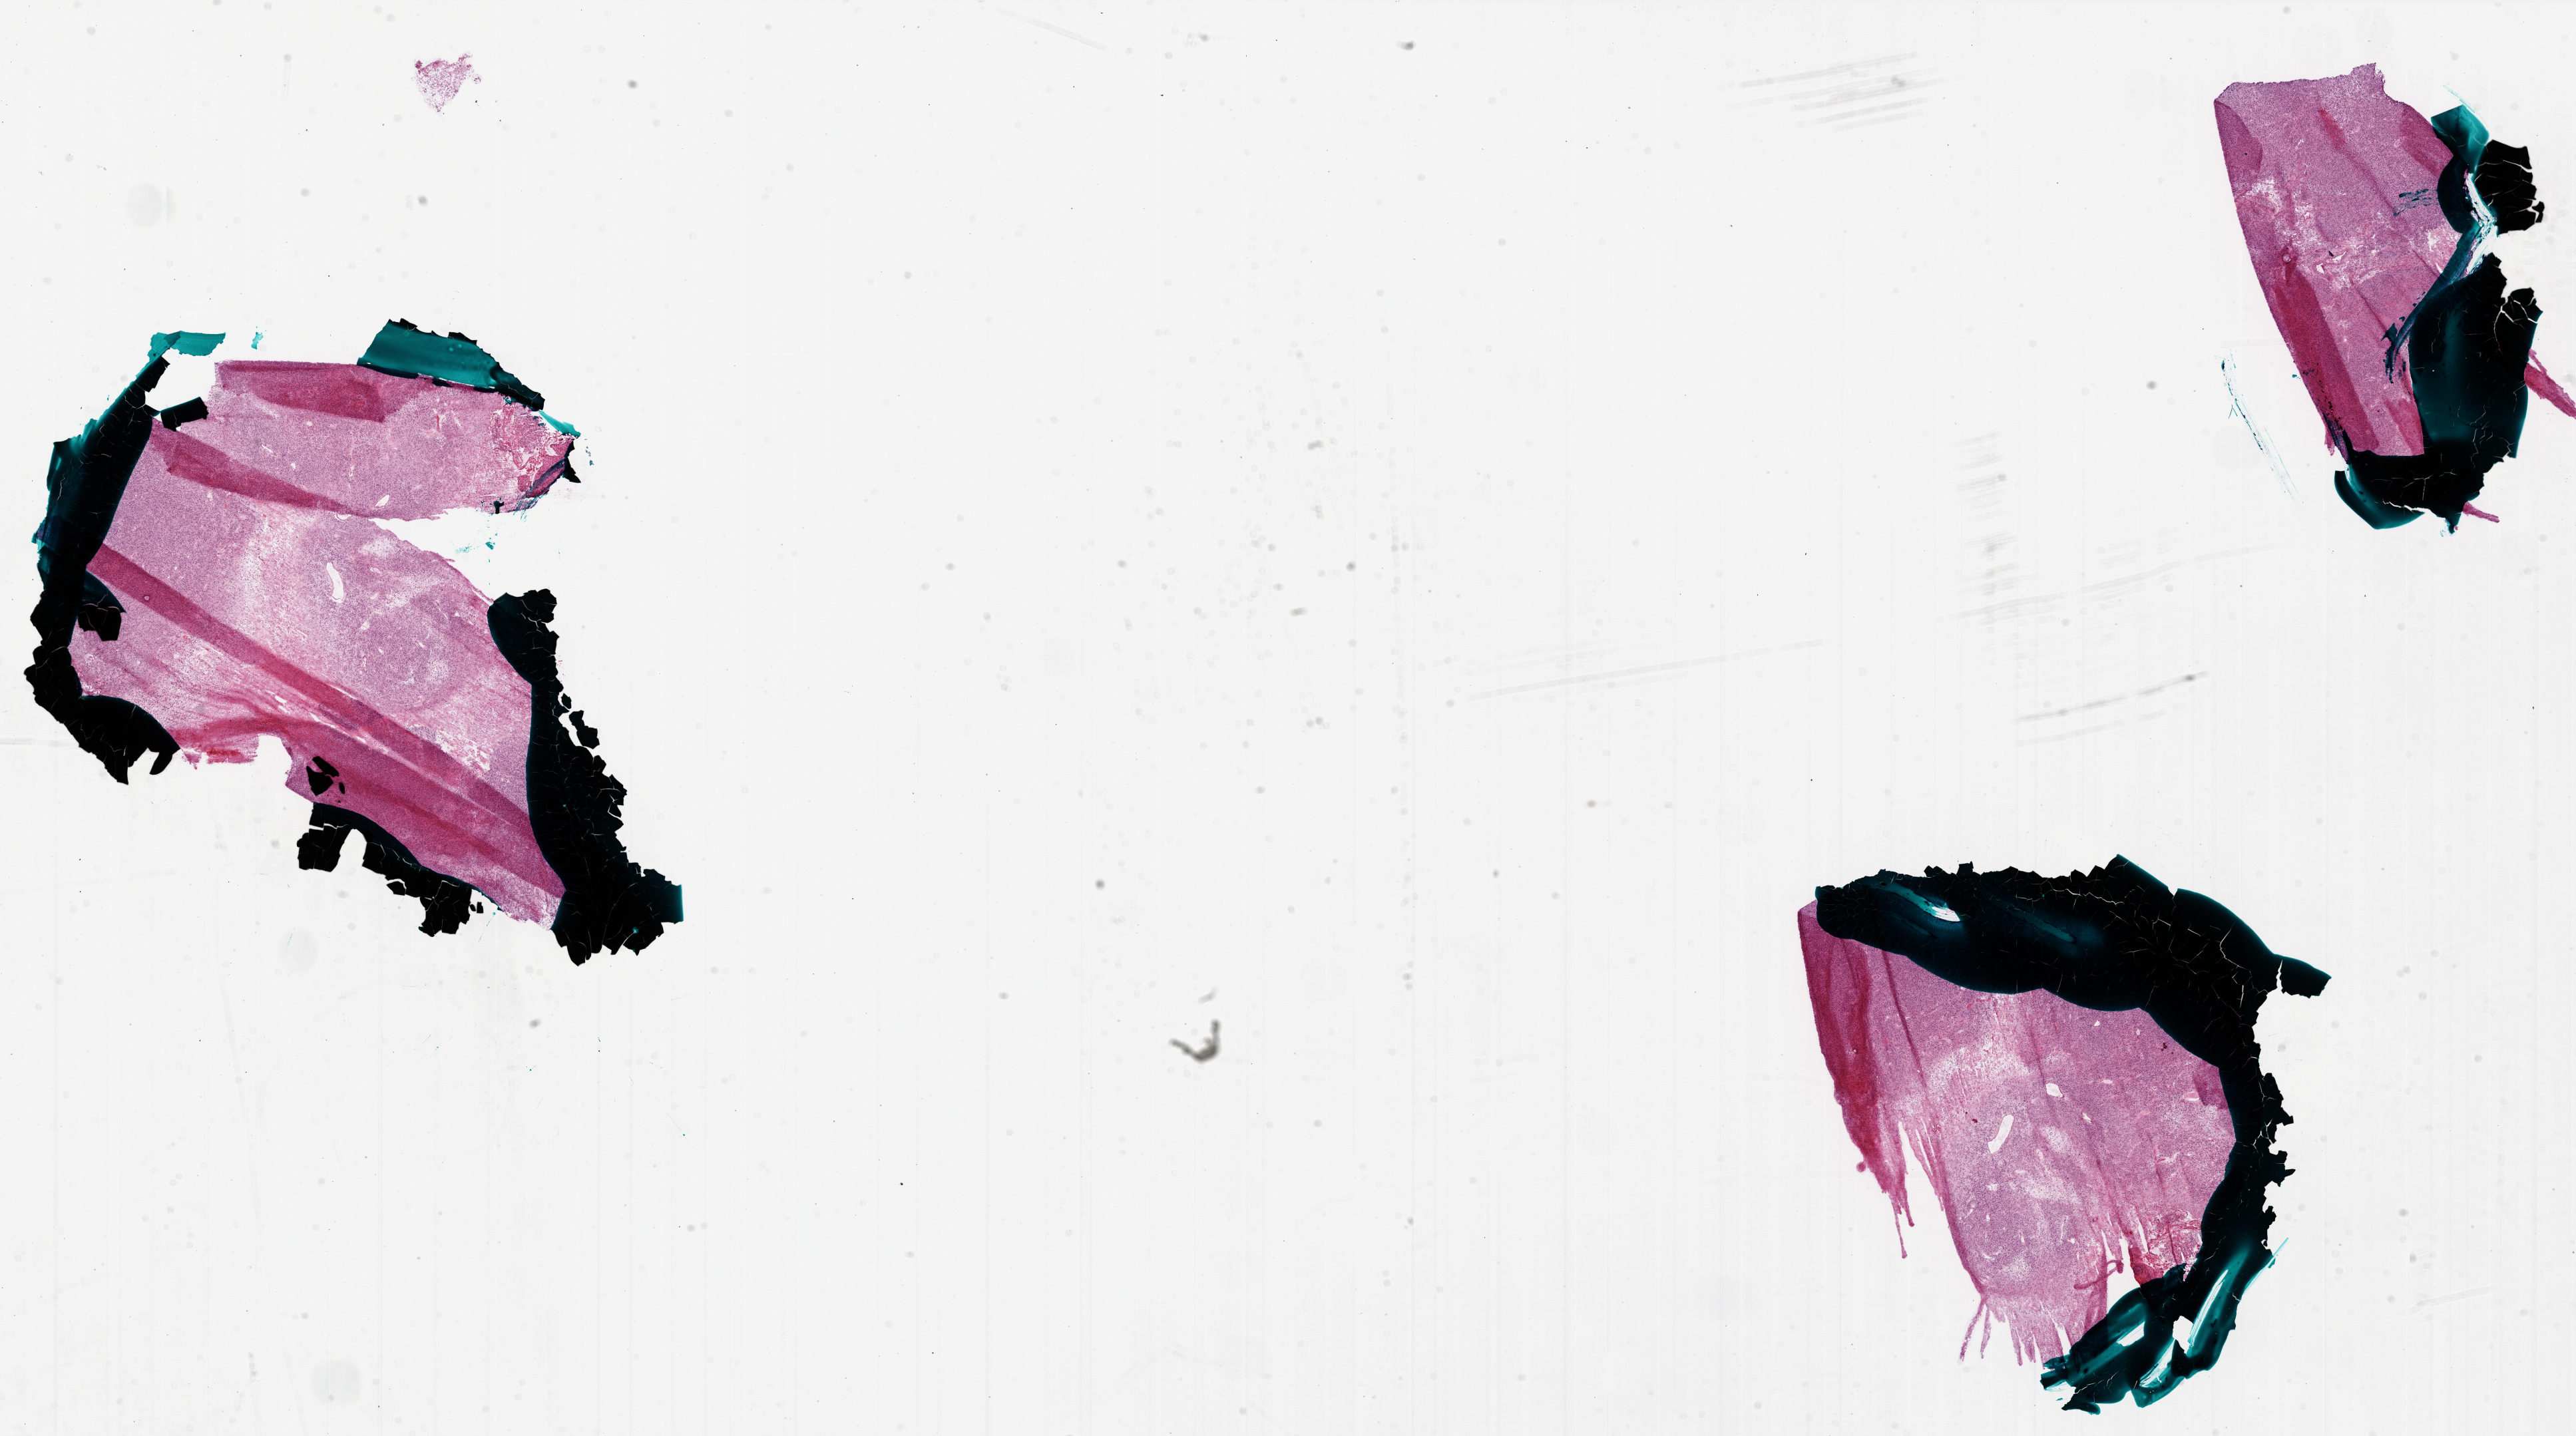
Digitized H&E tissue section (whole slide) — low-resolution overview of the scanned area, about 31.0 x 17.3 mm (slide scanned at 20x); frozen section; sample: primary tumour, brain. Male patient; age at initial diagnosis 76 years. Slide review estimates, as recorded: tumour cells 80%, tumour nuclei 100%, normal cells 0%, stromal cells 0%, necrosis 20%. Infiltration values recorded for this section: lymphocyte infiltration 0%, monocyte infiltration 0%, neutrophil infiltration 0%.
Diagnosis: Glioblastoma.